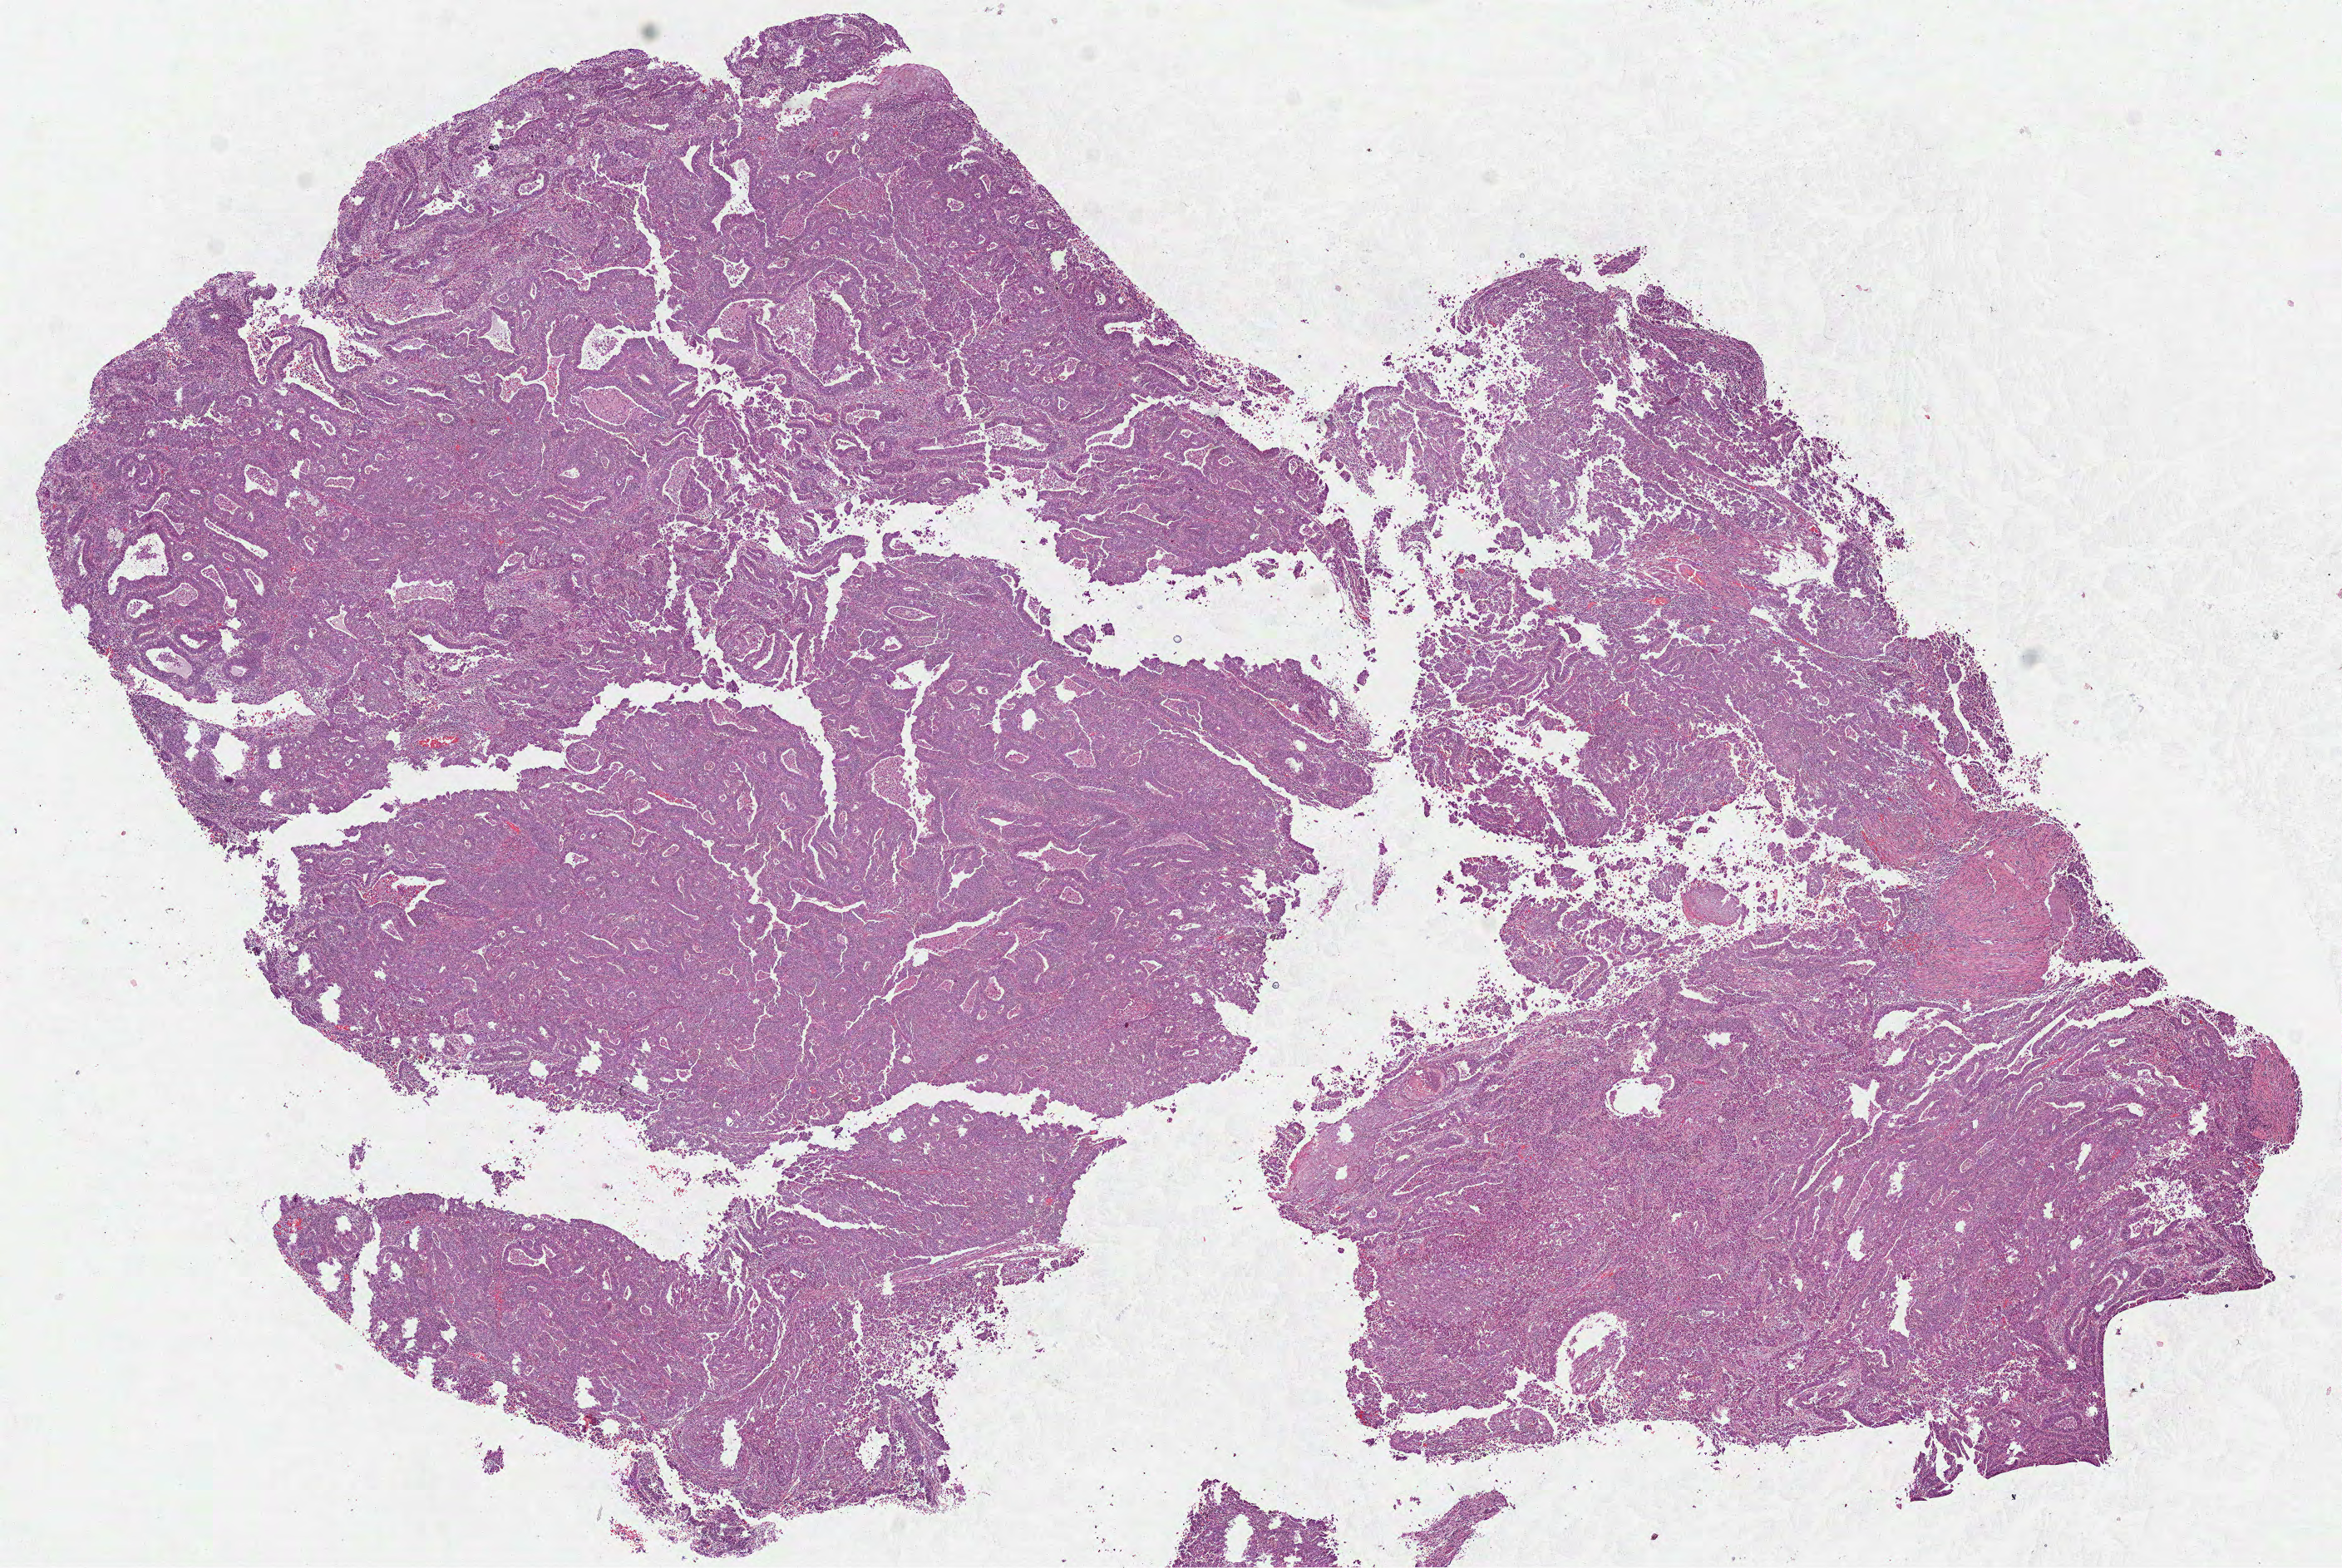
H&E whole-slide image — shown as a low-resolution overview of the whole scanned area (about 11.4 x 7.6 mm, slide scanned at 40x); formalin-fixed paraffin-embedded (FFPE) diagnostic section; uterus, primary tumour sample. Female, age 68 years at initial diagnosis. Histologic grade: G3 (poorly differentiated).
• FIGO stage: IC
• pathologic diagnosis: Endometrioid adenocarcinoma, NOS